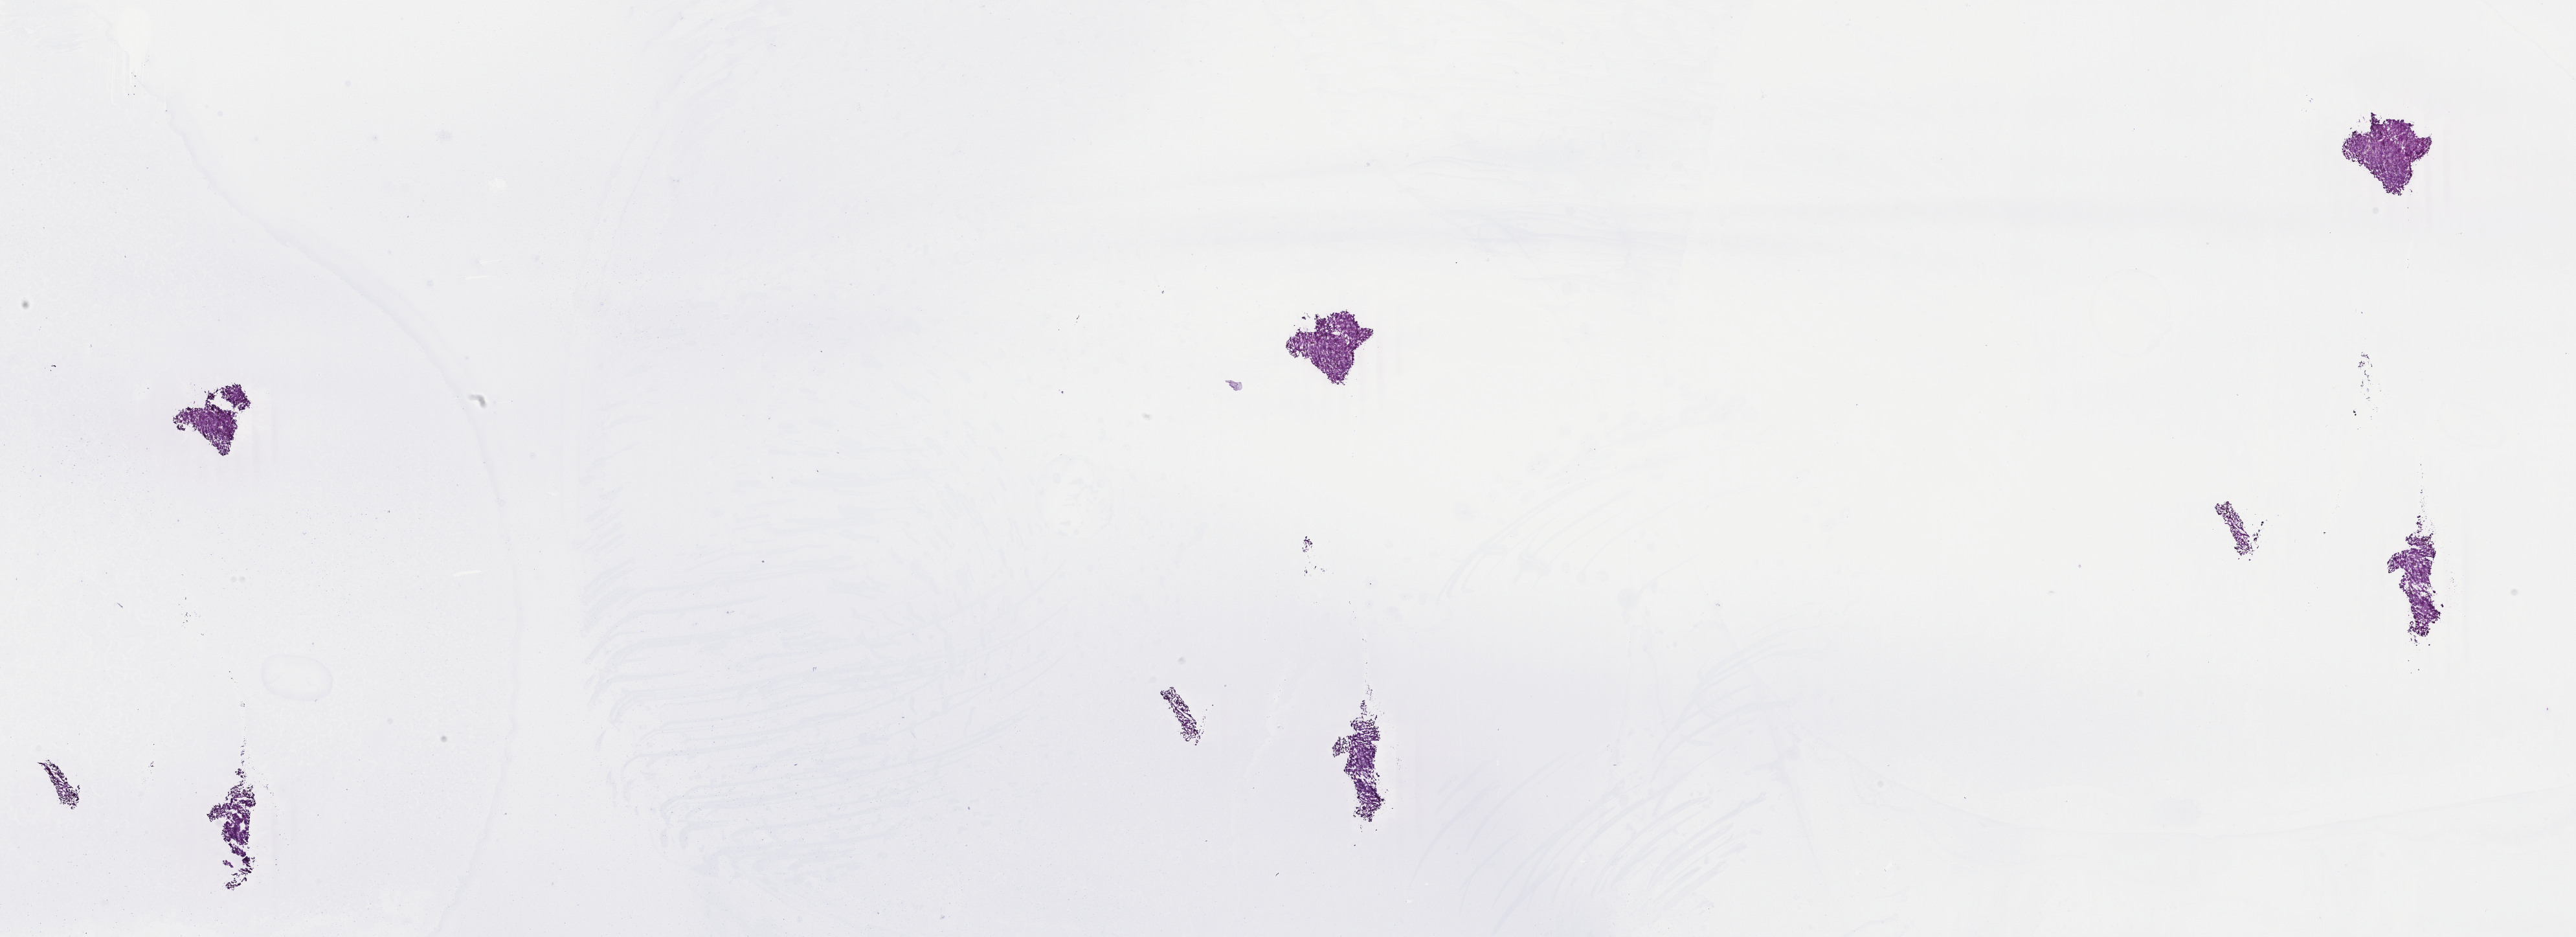
Whole-slide histology image, Hematoxylin and eosin (H&E) stained — shown as a low-resolution overview of the whole scanned area (about 31.6 x 11.5 mm). Frozen section. Sample: primary tumour, uvea. Male, age 59 years at initial diagnosis. Pathologist review of this section (percent, as recorded): tumour cells 100%, tumour nuclei 95%, normal cells 0%, stromal cells 0%, necrosis 0%. Inflammatory infiltration, as recorded: lymphocyte infiltration 0%, monocyte infiltration 0%, neutrophil infiltration 0%.
• diagnosis: Mixed epithelioid and spindle cell melanoma (choroid)